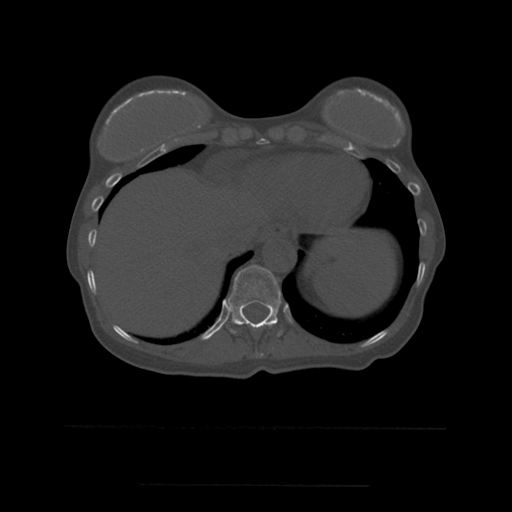
CT including the spine, one axial slice; slice 288 of 544 in the series (ordered by position); bone window (W 1800 / L 400 HU); 1.25 mm slice thickness; 512 × 512 image matrix, field of view 350 × 350 mm. Patient age 58 years. From the clinical record (not read from this slice): primary cancer: lung.
Annotated regions visible in this slice (semi-automatically segmented with operator editing):
- T10 vertebra: bounding box [x1, y1, x2, y2] px = [243, 320, 278, 356]
- T11 vertebra: [225, 265, 281, 337]